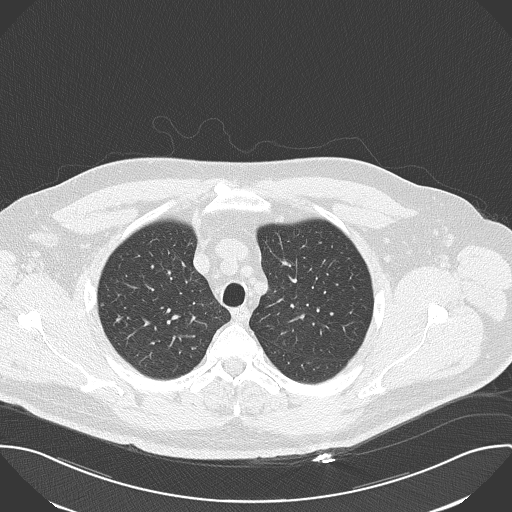
Axial slice from a low-dose chest CT screening exam. Baseline screening round. Lung window (W 1500 / L -600 HU). 2 mm slice thickness. Lung (sharp) reconstruction kernel (B50f). Slice 37 of 156 in the series. 512 × 512 image matrix. Male, age 56 years at enrolment.
Lesion marked by an expert reader, bounding box (x1, y1, x2, y2) in pixels: (96, 300, 131, 337). No non-calcified nodule or mass ≥4 mm was recorded by the screening reader at this exam. Official screen result: negative screen, minor abnormalities not suspicious for lung cancer. Participant outcome: lung cancer diagnosed 476 days after this screen — squamous cell carcinoma, NOS, right upper lobe, moderately differentiated (G2), stage IA (AJCC 6th edition), 10 mm at pathology.